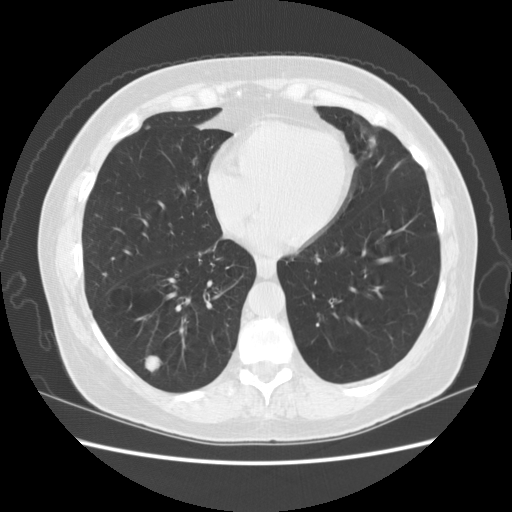
Low-dose screening chest CT, one axial slice; reconstruction kernel STANDARD; 120 kVp; lung window (W 1500 / L -600 HU); 2.5 mm slice thickness; 512 × 512 image matrix.
Structures marked on this image (expert manual segmentation):
- lesion 1 (tumor, lower lobe of right lung): bounding box [x1, y1, x2, y2] px = [146, 356, 159, 371]